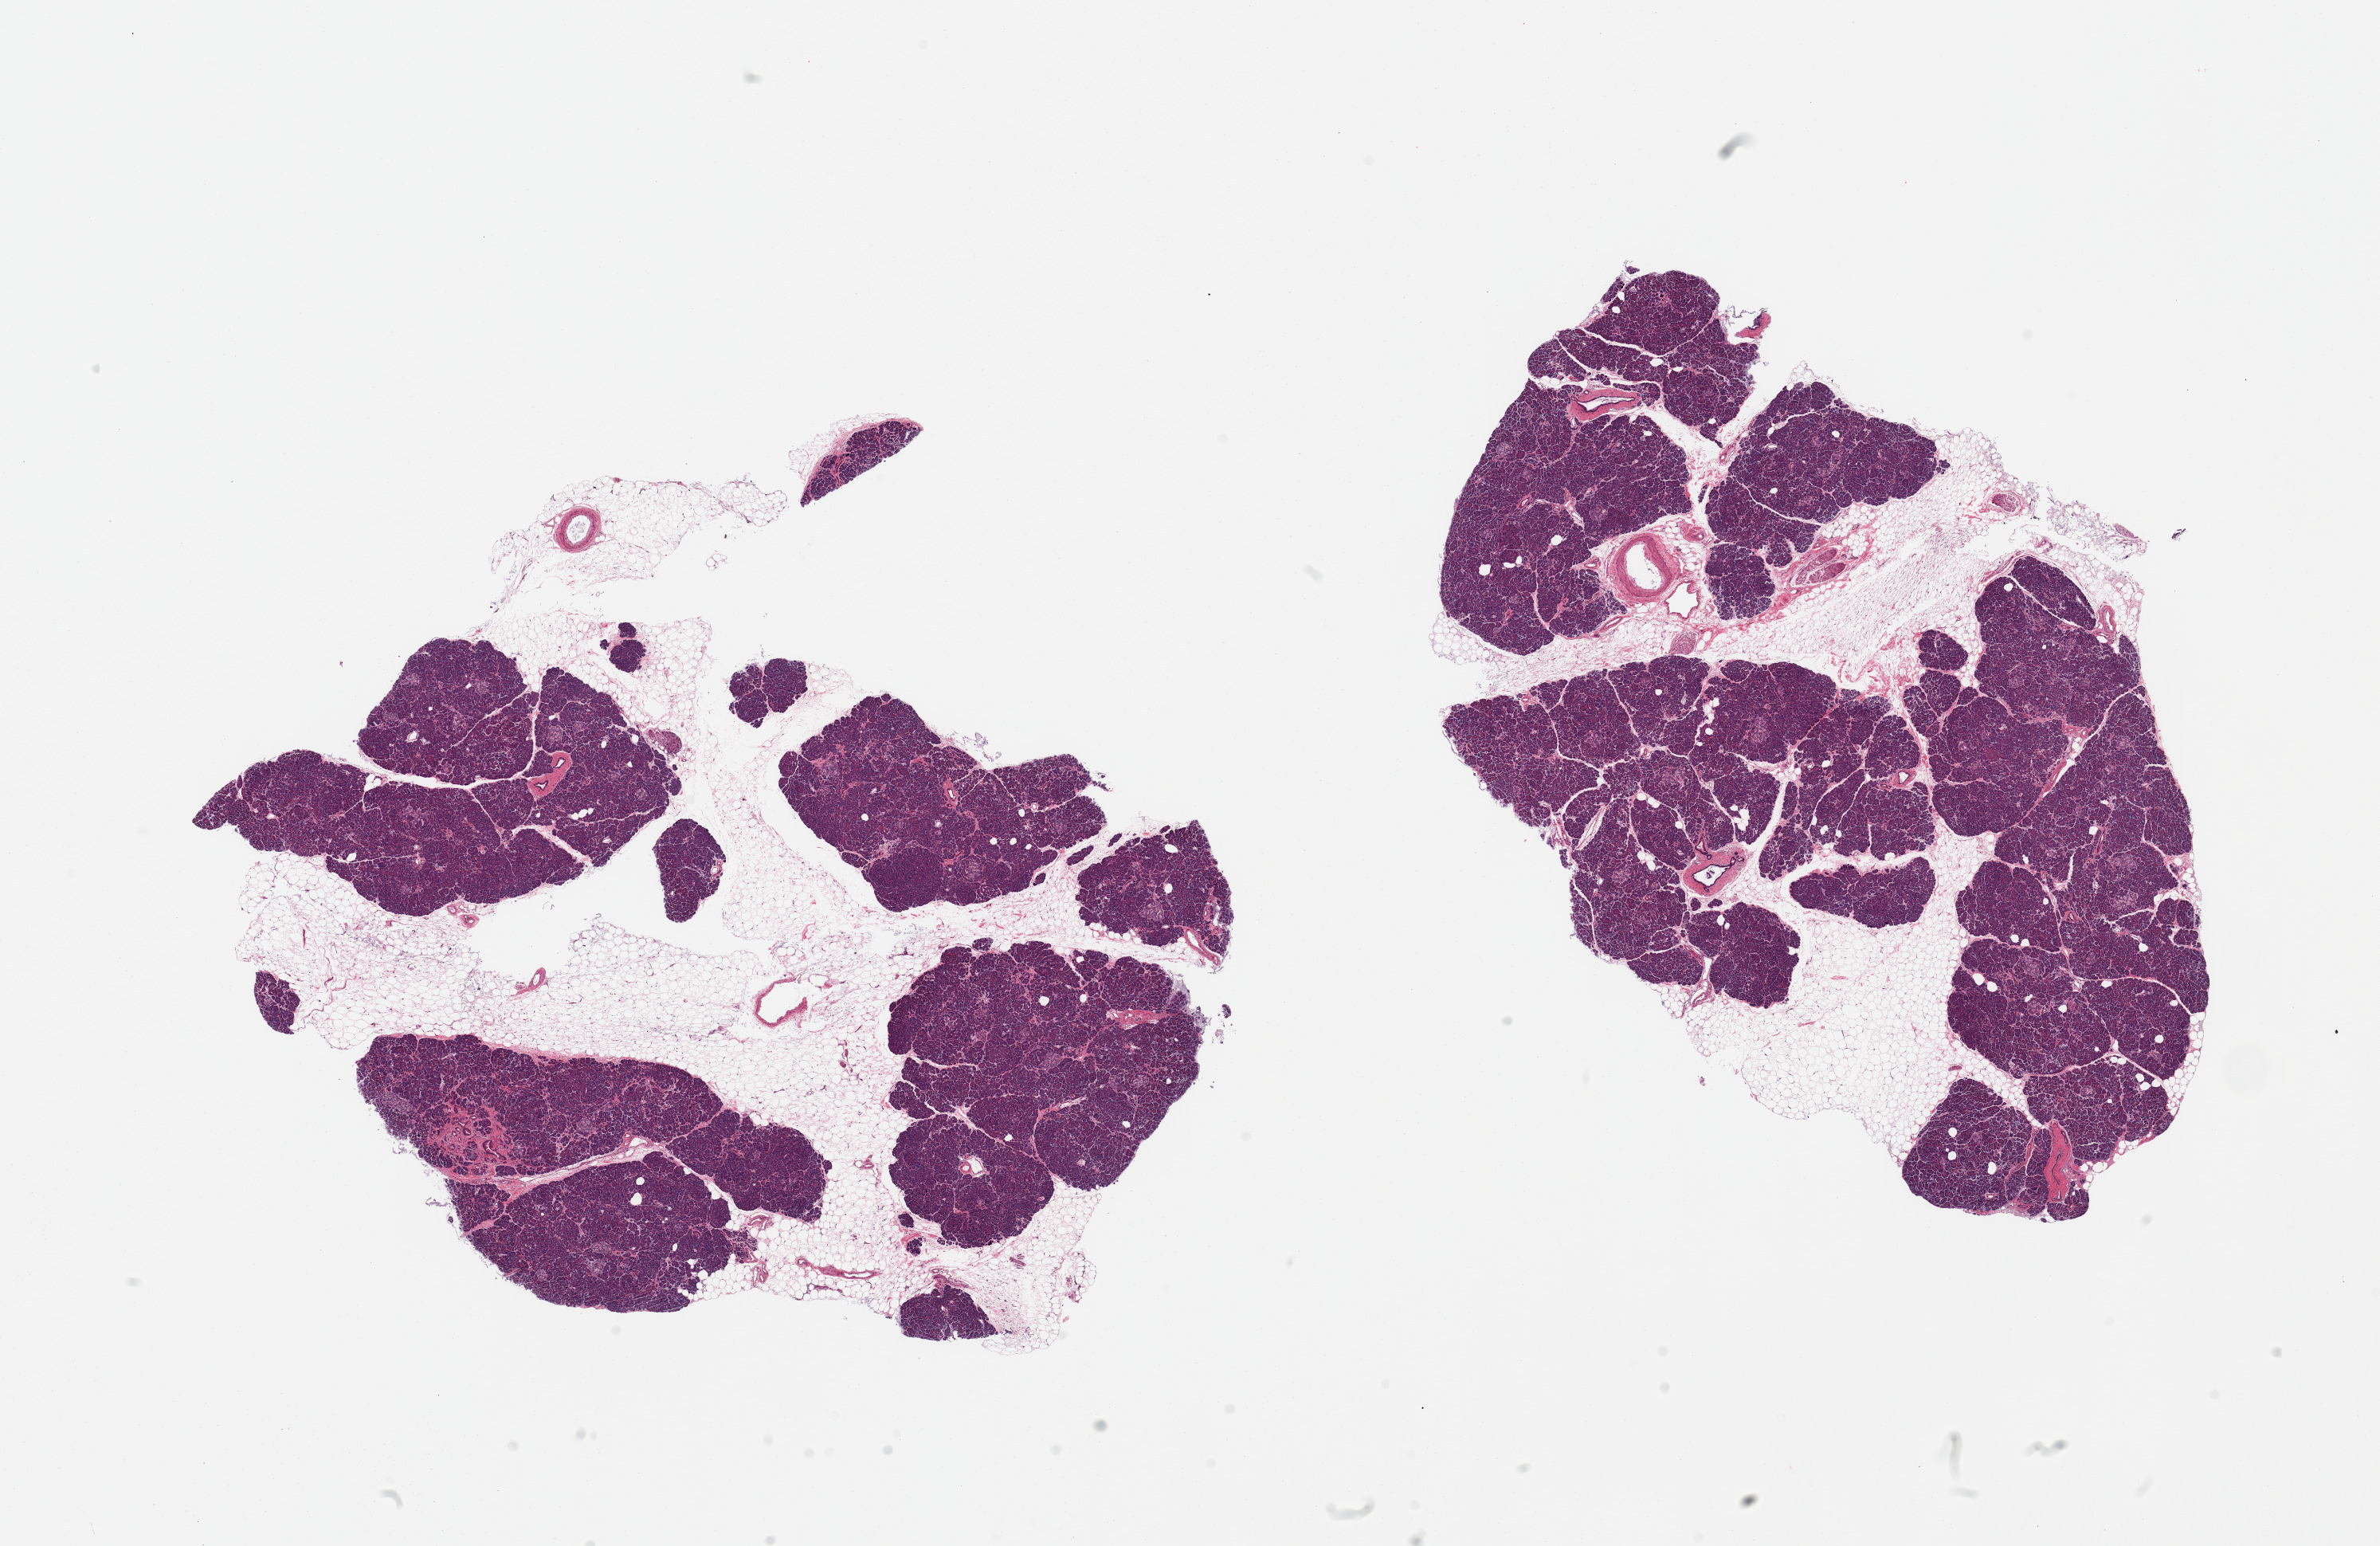
Hematoxylin and eosin (H&E) whole-slide image, brightfield — a low-resolution overview of the entire scanned area, about 23.6 x 15.3 mm. PAXgene-fixed, paraffin-embedded tissue. Sampled site (target tissue): pancreas. Tissue donor sample.
* pathologist's review note for this sample: 2 pieces, ~40% interstitial fat; Islets well preserved, moderate numbers